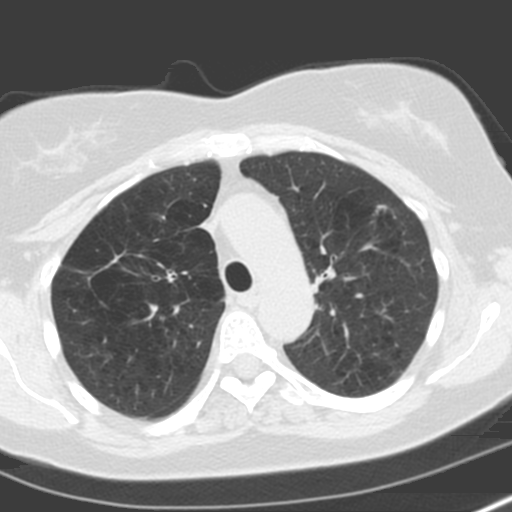
Chest CT (low-dose screening protocol), one axial image; baseline annual screen; lung window (W 1500 / L -600 HU); 3.2 mm slice thickness; slice 51 of 173 in the series; 512 × 512 image matrix. Female participant, aged 57 years at enrolment. Former smoker at enrolment.
• Expert reader's lesion annotation, bounding box (x1, y1, x2, y2) in pixels: (359, 201, 399, 232).
• No non-calcified nodule or mass ≥4 mm was recorded by the screening reader at this exam.
• Official screen result: negative screen, minor abnormalities not suspicious for lung cancer.
• Later outcome: lung cancer diagnosed 503 days after this screen — adenocarcinoma, NOS, left upper lobe, moderately differentiated (G2), stage IA (AJCC 6th edition), 18 mm at pathology.